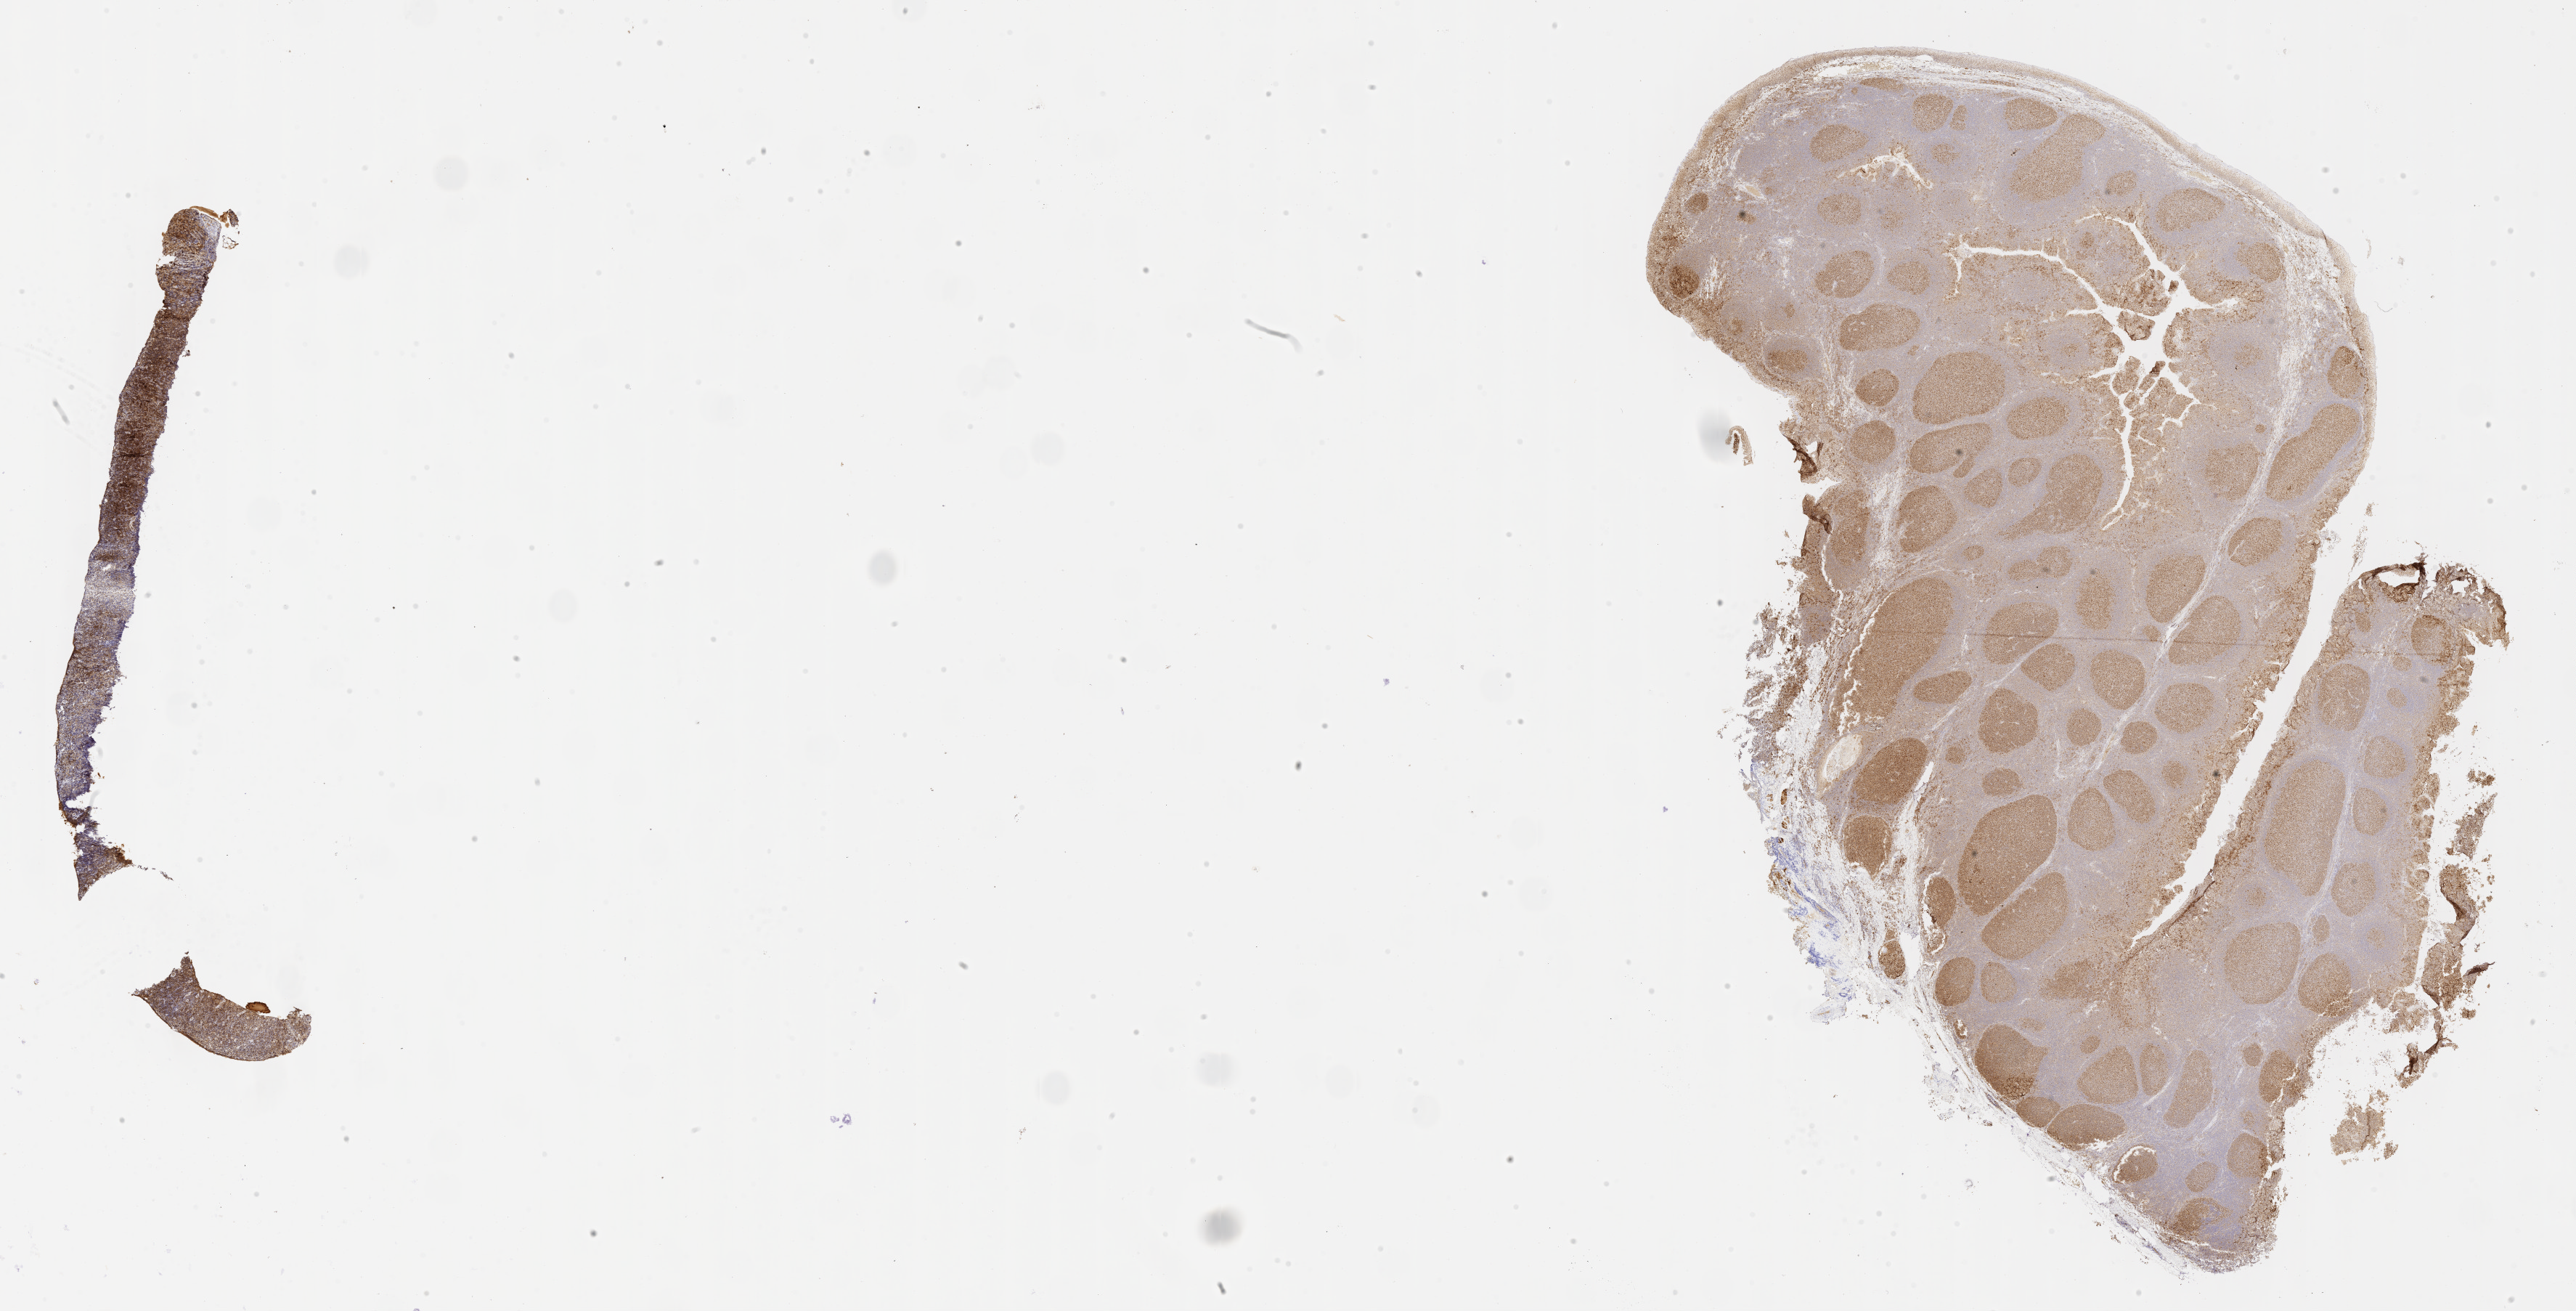
Whole-slide image, immunohistochemical stain for BCL6, whole scanned area (about 28.7 x 14.6 mm) shown as a low-resolution overview. Tumor tissue. Anatomic site: ovary. Patient: female, age at initial diagnosis 9 years.
* histologic diagnosis: Burkitt lymphoma, NOS